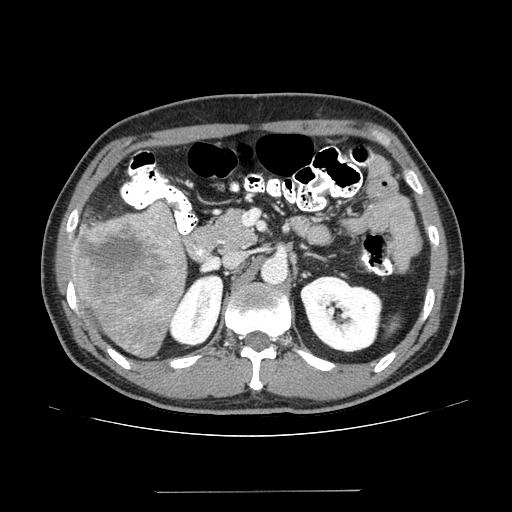
Contrast-enhanced abdominal CT (liver protocol), one axial slice; slice 68 of 131 in the series (ordered by position); reconstruction kernel STANDARD; 100 kVp; one of 2 acquisitions stored at this slice position; soft-tissue window (W 400 / L 40 HU); 2.5 mm slice thickness; 512 × 512 image matrix. Case-level facts recorded for this patient, not image findings: diagnosis: hepatocellular carcinoma (patient treated with transarterial chemoembolisation; whether this scan precedes or follows treatment is not stated here); TNM stage (as recorded): Stage-I; Child-Pugh class: A; tumour differentiation: poorly differentiated; tumour nodularity: uninodular.
Annotated regions visible in this slice (semi-automatic segmentation, software-assisted and operator-edited):
- liver parenchyma outside the tumour (the mass and vessels are separate outlines, so this box may not span the whole liver): bounding box (x1, y1, x2, y2) in pixels: (69, 202, 186, 356)
- mass: (73, 212, 184, 325)